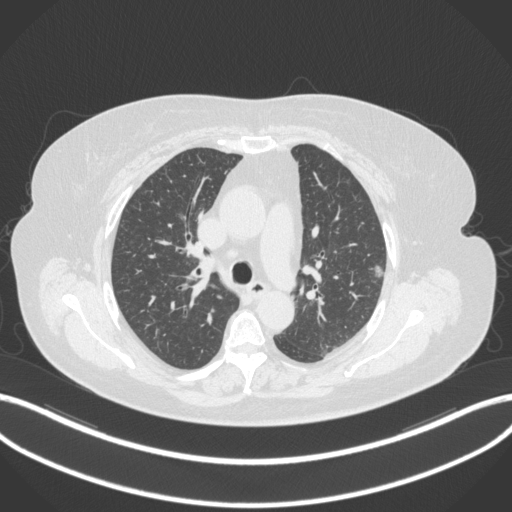
Chest CT, one axial slice. Slice 214 of 310 in the series (ordered by position). Reconstruction kernel B31f. Lung window (W 1500 / L -600 HU). 1 mm slice thickness. 512 × 512 image matrix. Female patient, age 70 years. From the clinical record (not read from this slice): clinical TNM (as recorded): T1c N0 M0.
Structures marked on this image (bounding box drawn by a radiologist):
- lung tumour (recorded histology: adenocarcinoma): bounding box <369,262,388,286> (left, top, right, bottom; pixels)